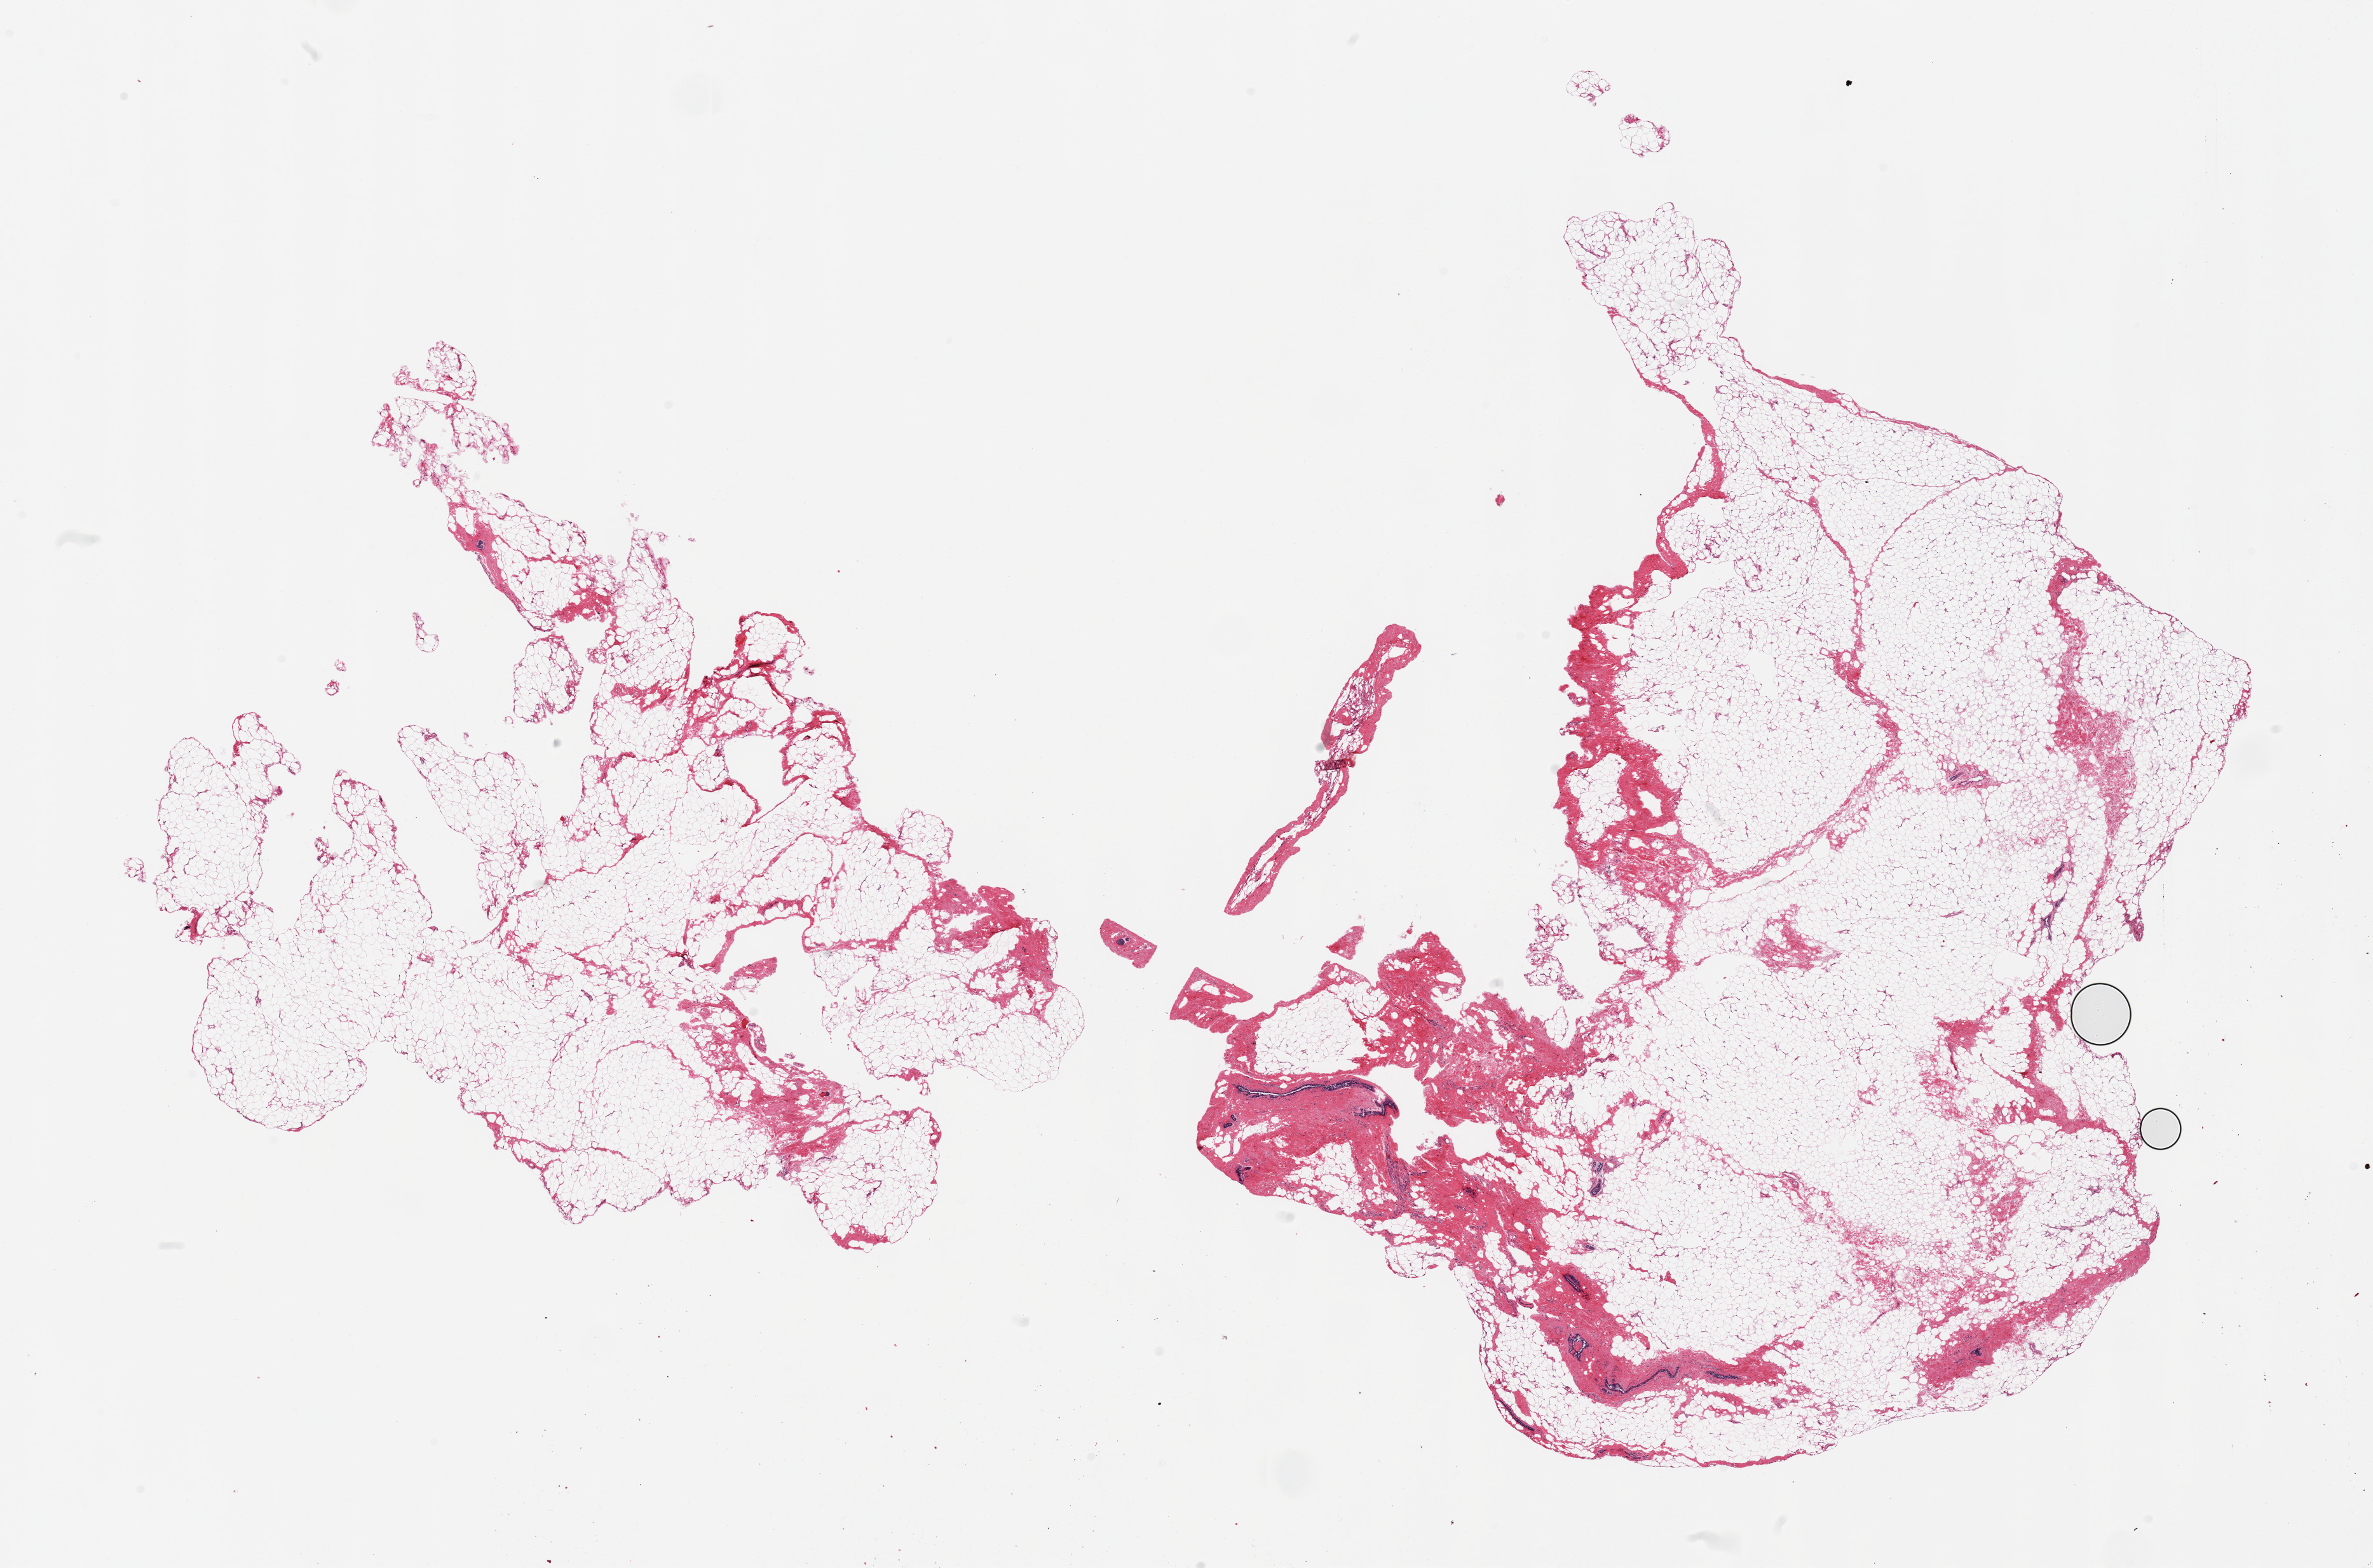
Whole-slide image, H&E stain — shown as a low-resolution overview of the whole scanned area (about 29.5 x 19.5 mm, acquisition: 20x scan); PAXgene-fixed paraffin-embedded (PFPE) section; section of breast (target tissue); tissue donor sample. Female donor.
Pathologist's review note for this sample: 2 pieces; mostly fibroadipose tisue with ductal structures.